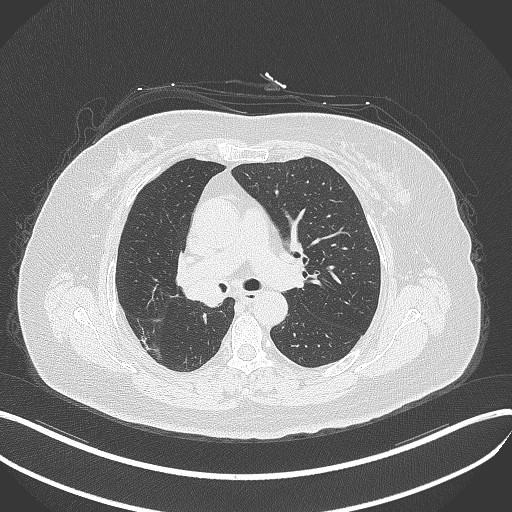
Chest CT, one axial slice. Slice 223 of 376 in the series (ordered by position). Reconstruction kernel B70f. Lung window (W 1500 / L -600 HU). 512 × 512 image matrix. Female patient, age 60 years. From the clinical record (not read from this slice): clinical TNM (as recorded): T1c N0 M0.
Outlined on this slice (rectangle marked by the reading radiologist):
- lung tumour (recorded histology: squamous cell carcinoma): box from (x=180, y=263) to (x=223, y=309) px